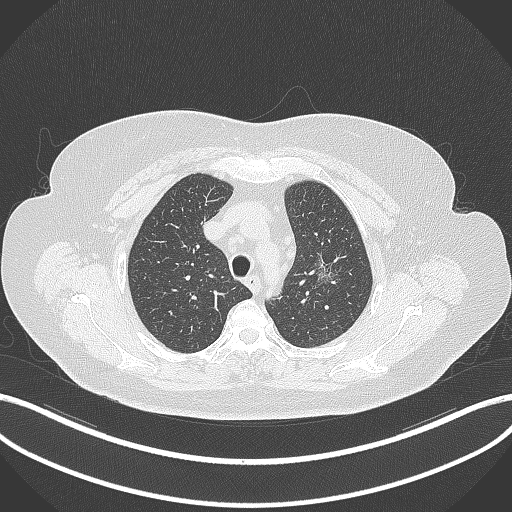
Chest CT, one axial slice. Slice 265 of 309 in the series (ordered by position). Reconstruction kernel B70f. Lung window (W 1500 / L -600 HU). 1 mm slice thickness. 512 × 512 image matrix, field of view 400 × 400 mm. Patient: female, 70 years. Case-level facts recorded for this patient, not image findings: clinical TNM (as recorded): T1c N0 M0.
Annotated regions visible in this slice (rectangle marked by the reading radiologist):
- lung tumour (recorded histology: adenocarcinoma): bounding box (x1, y1, x2, y2) in pixels: (315, 252, 343, 290)